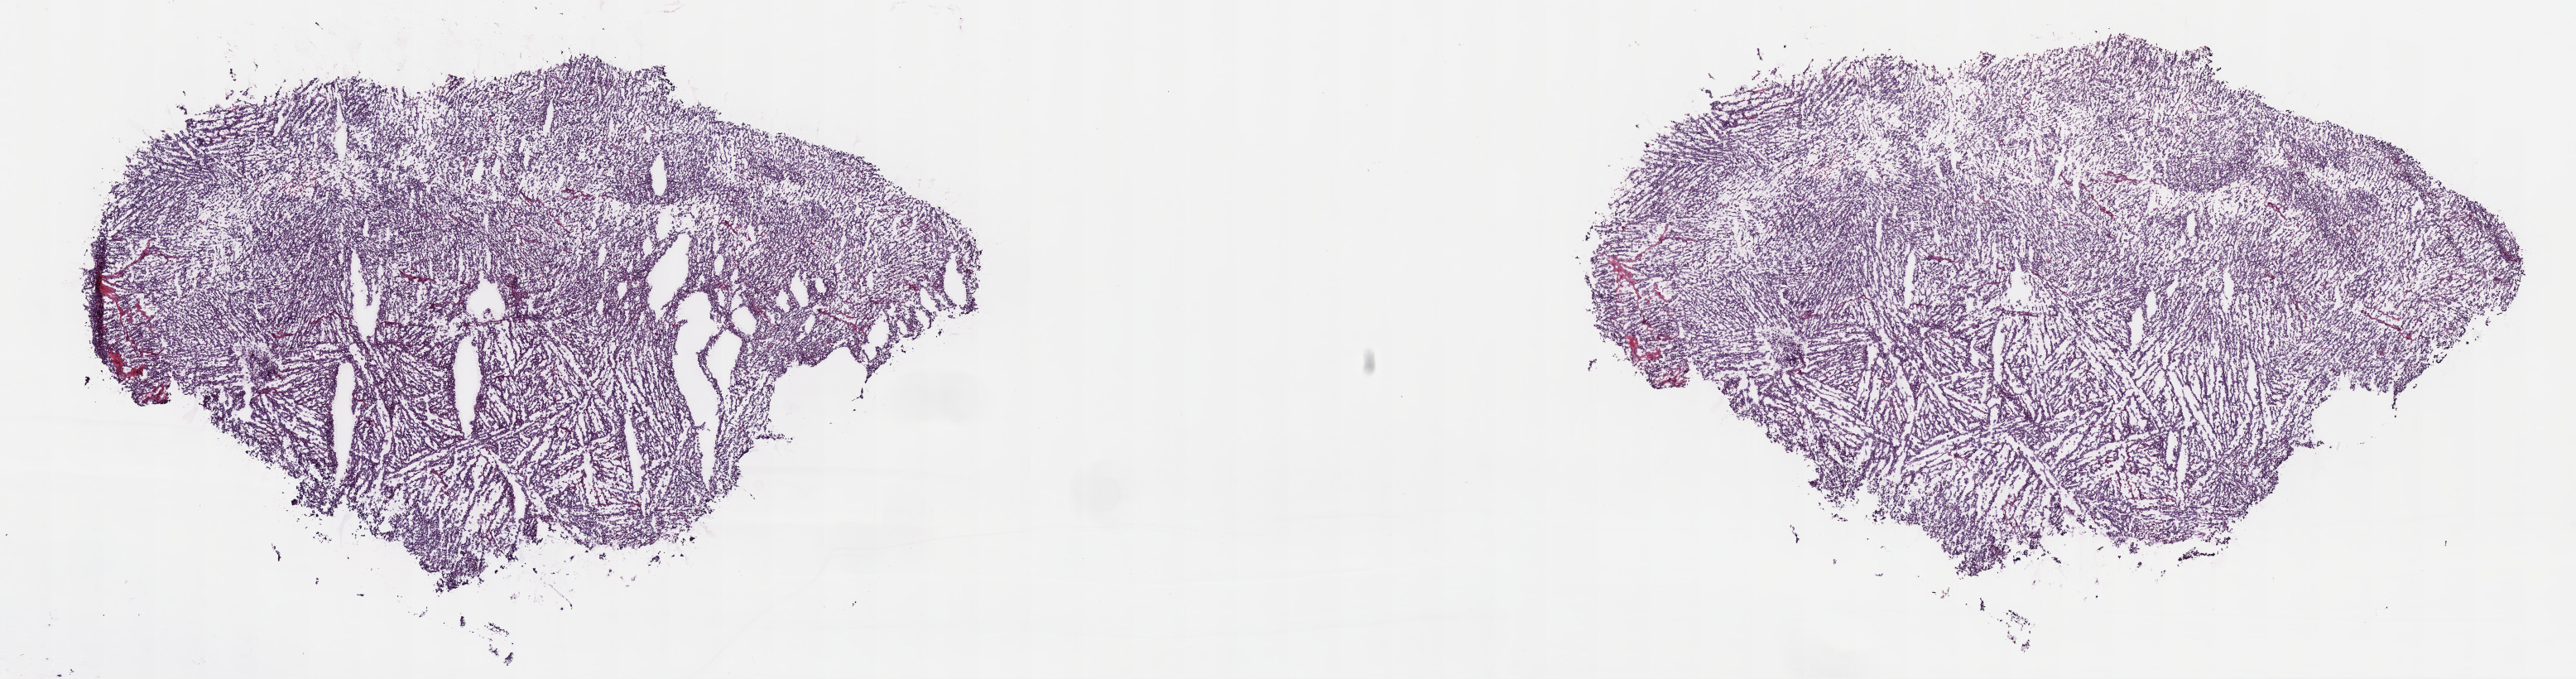
Whole-slide histology image, H&E-stained — shown as a low-resolution overview of the whole scanned area (about 25.2 x 6.6 mm). Frozen section from the top of the tissue portion. Primary tumour sample from the testis. Male patient; age at initial diagnosis 38 years. Slide review estimates, as recorded: tumour cells 90%, tumour nuclei 90%, normal cells 0%, stromal cells 10%, necrosis 0%. Infiltration values recorded for this section: lymphocyte infiltration 60%, monocyte infiltration 20%, neutrophil infiltration 10%.
• AJCC pathologic stage: I (6th edition)
• pathologic diagnosis: Seminoma, NOS